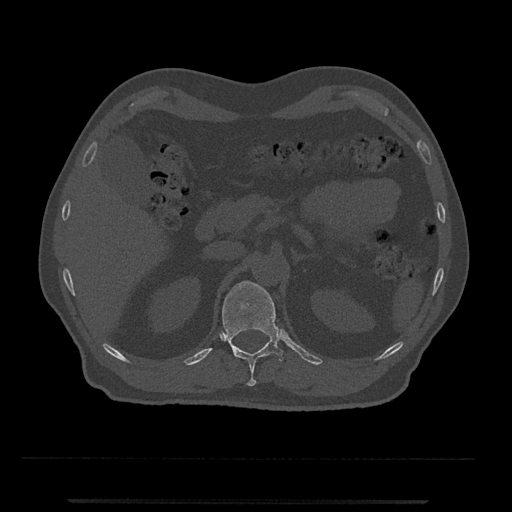
CT including the spine, one axial slice; position 397 of 797 along the scan axis; reconstruction kernel Br40s/3; 120 kVp; bone window (W 1800 / L 400 HU); 0.5 mm slice thickness; 512 × 512 image matrix, field of view 419 × 419 mm. Male patient, age 63 years. Case-level facts recorded for this patient, not image findings: primary cancer: prostate.
Outlined on this slice (semi-automatic segmentation, software-assisted and operator-edited):
- T12 vertebra: bounding box [x1, y1, x2, y2] px = [222, 281, 287, 386]